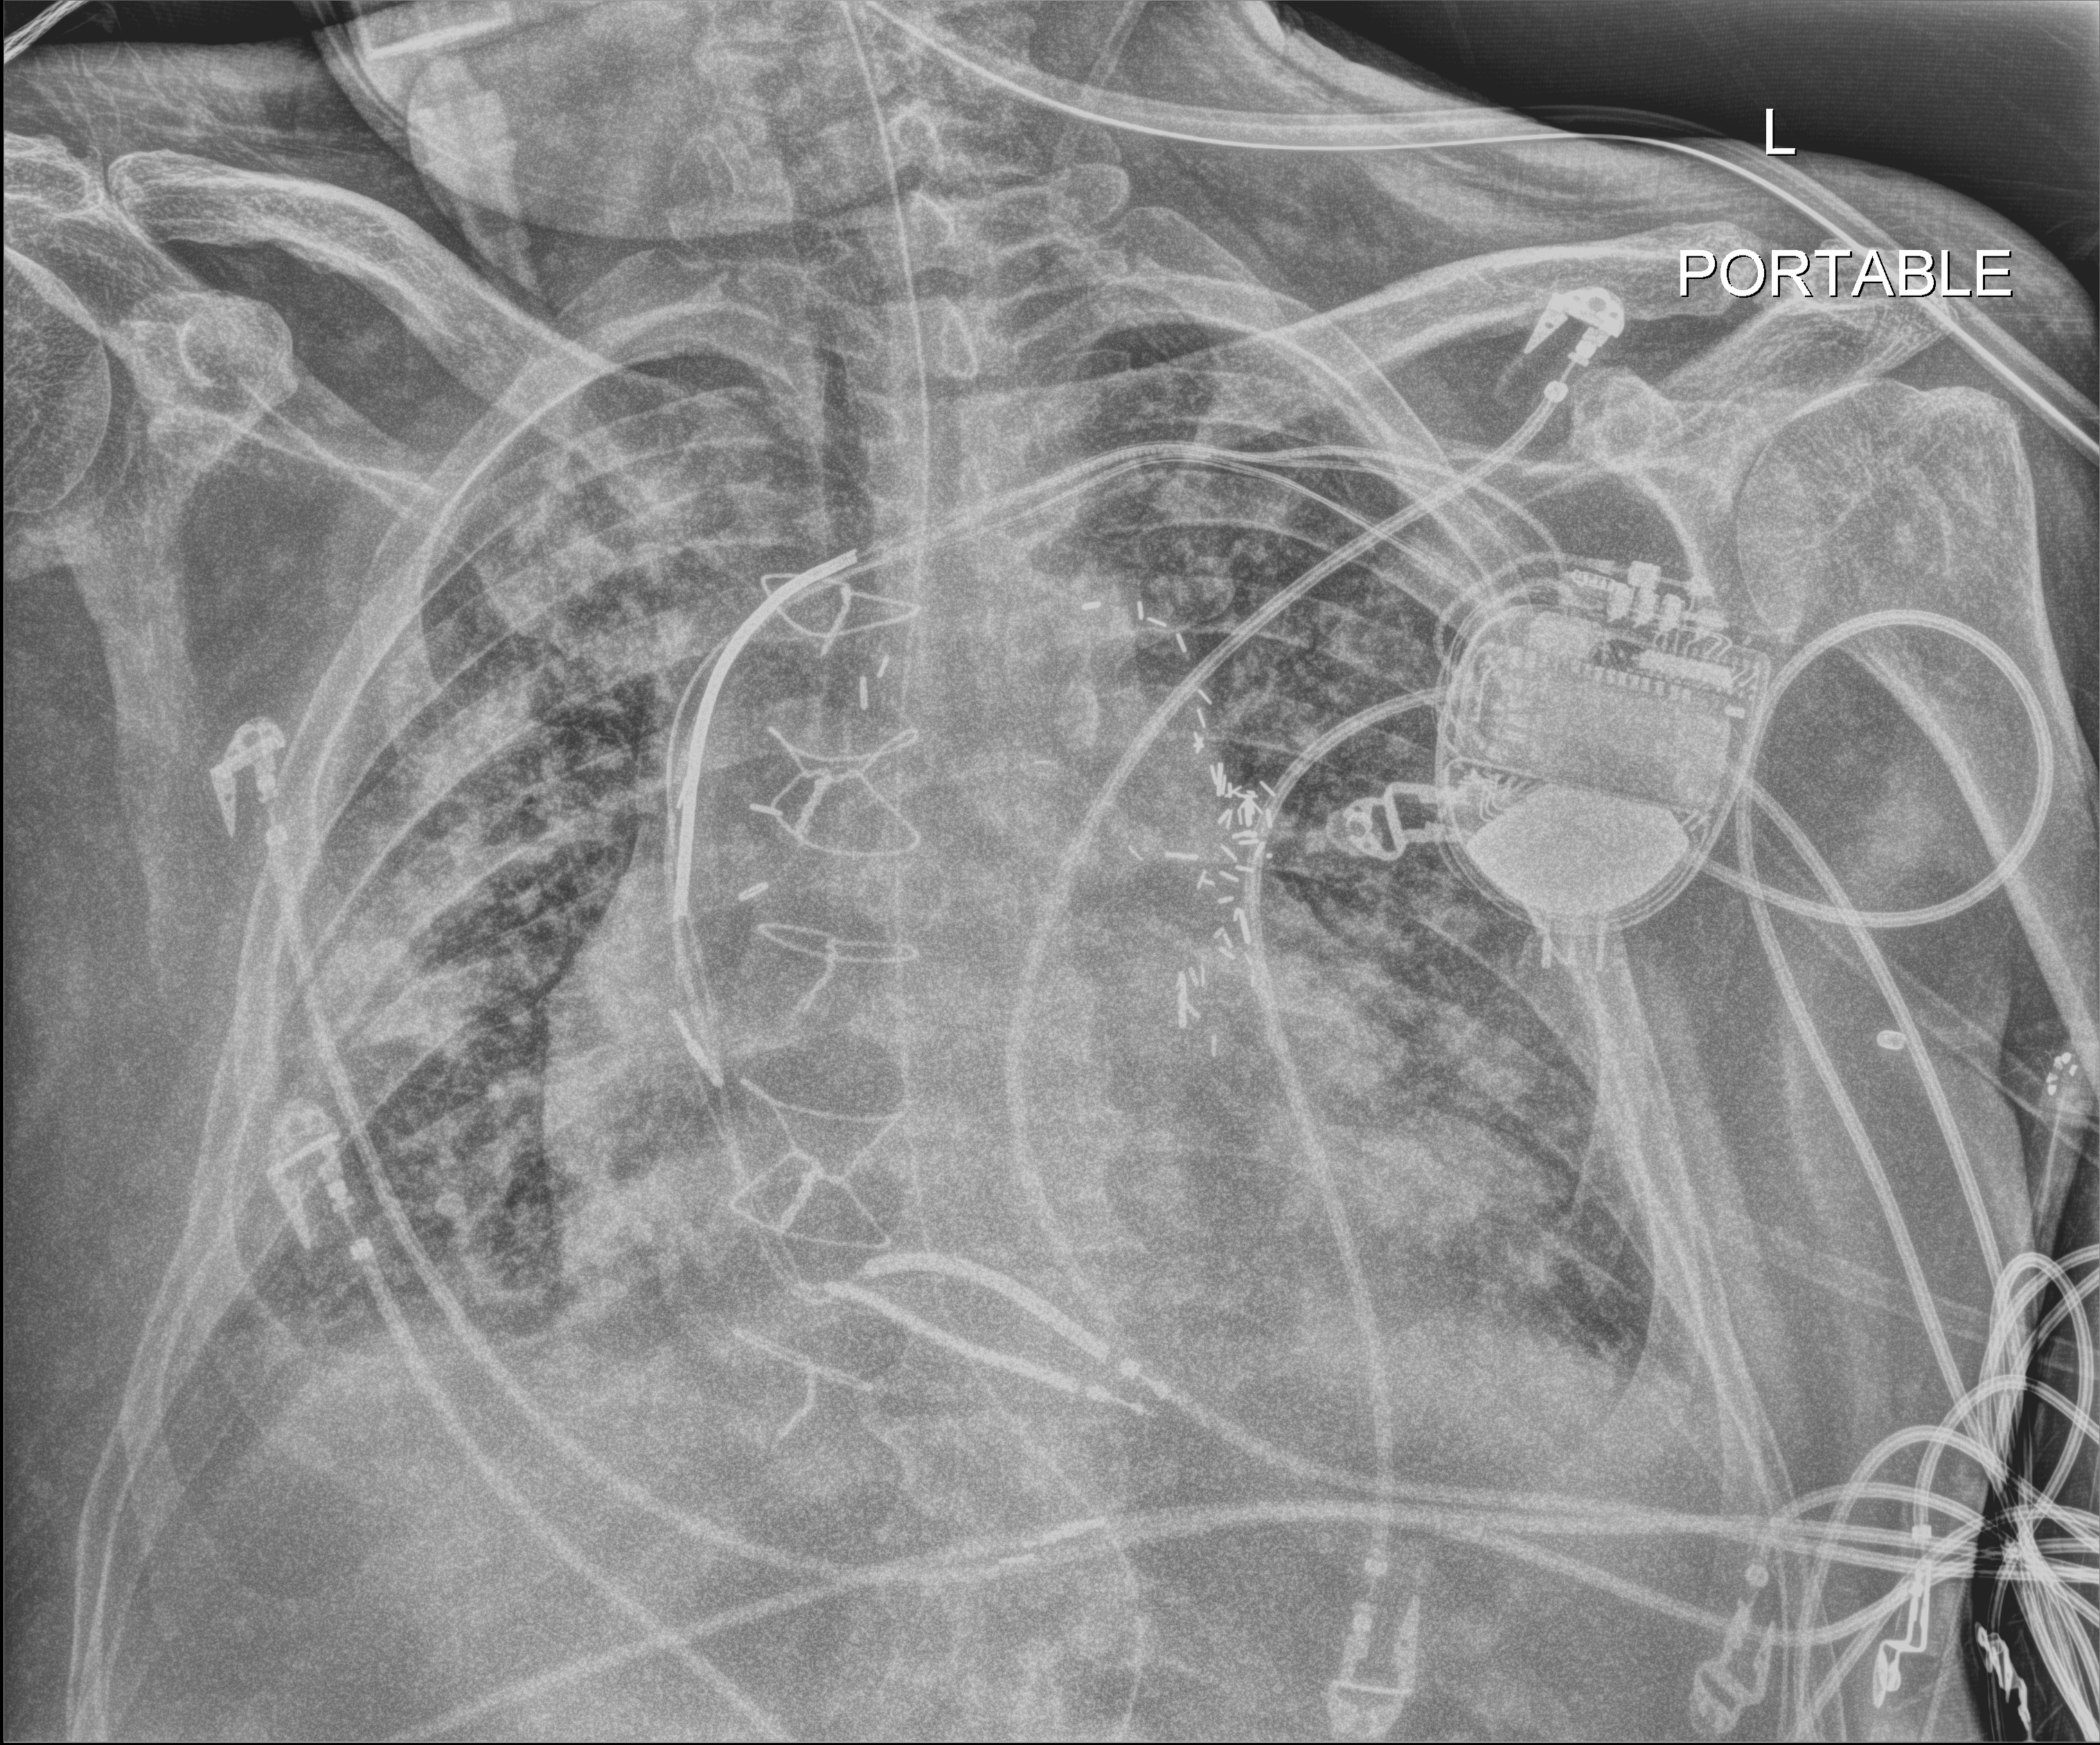
Portable chest radiograph; anteroposterior (AP) projection. Male patient hospitalised with COVID-19, age 60–74 years.
Hospital-stay facts (about this admission, not read from this image; timing relative to this image not recorded): diabetes (admission record): yes.